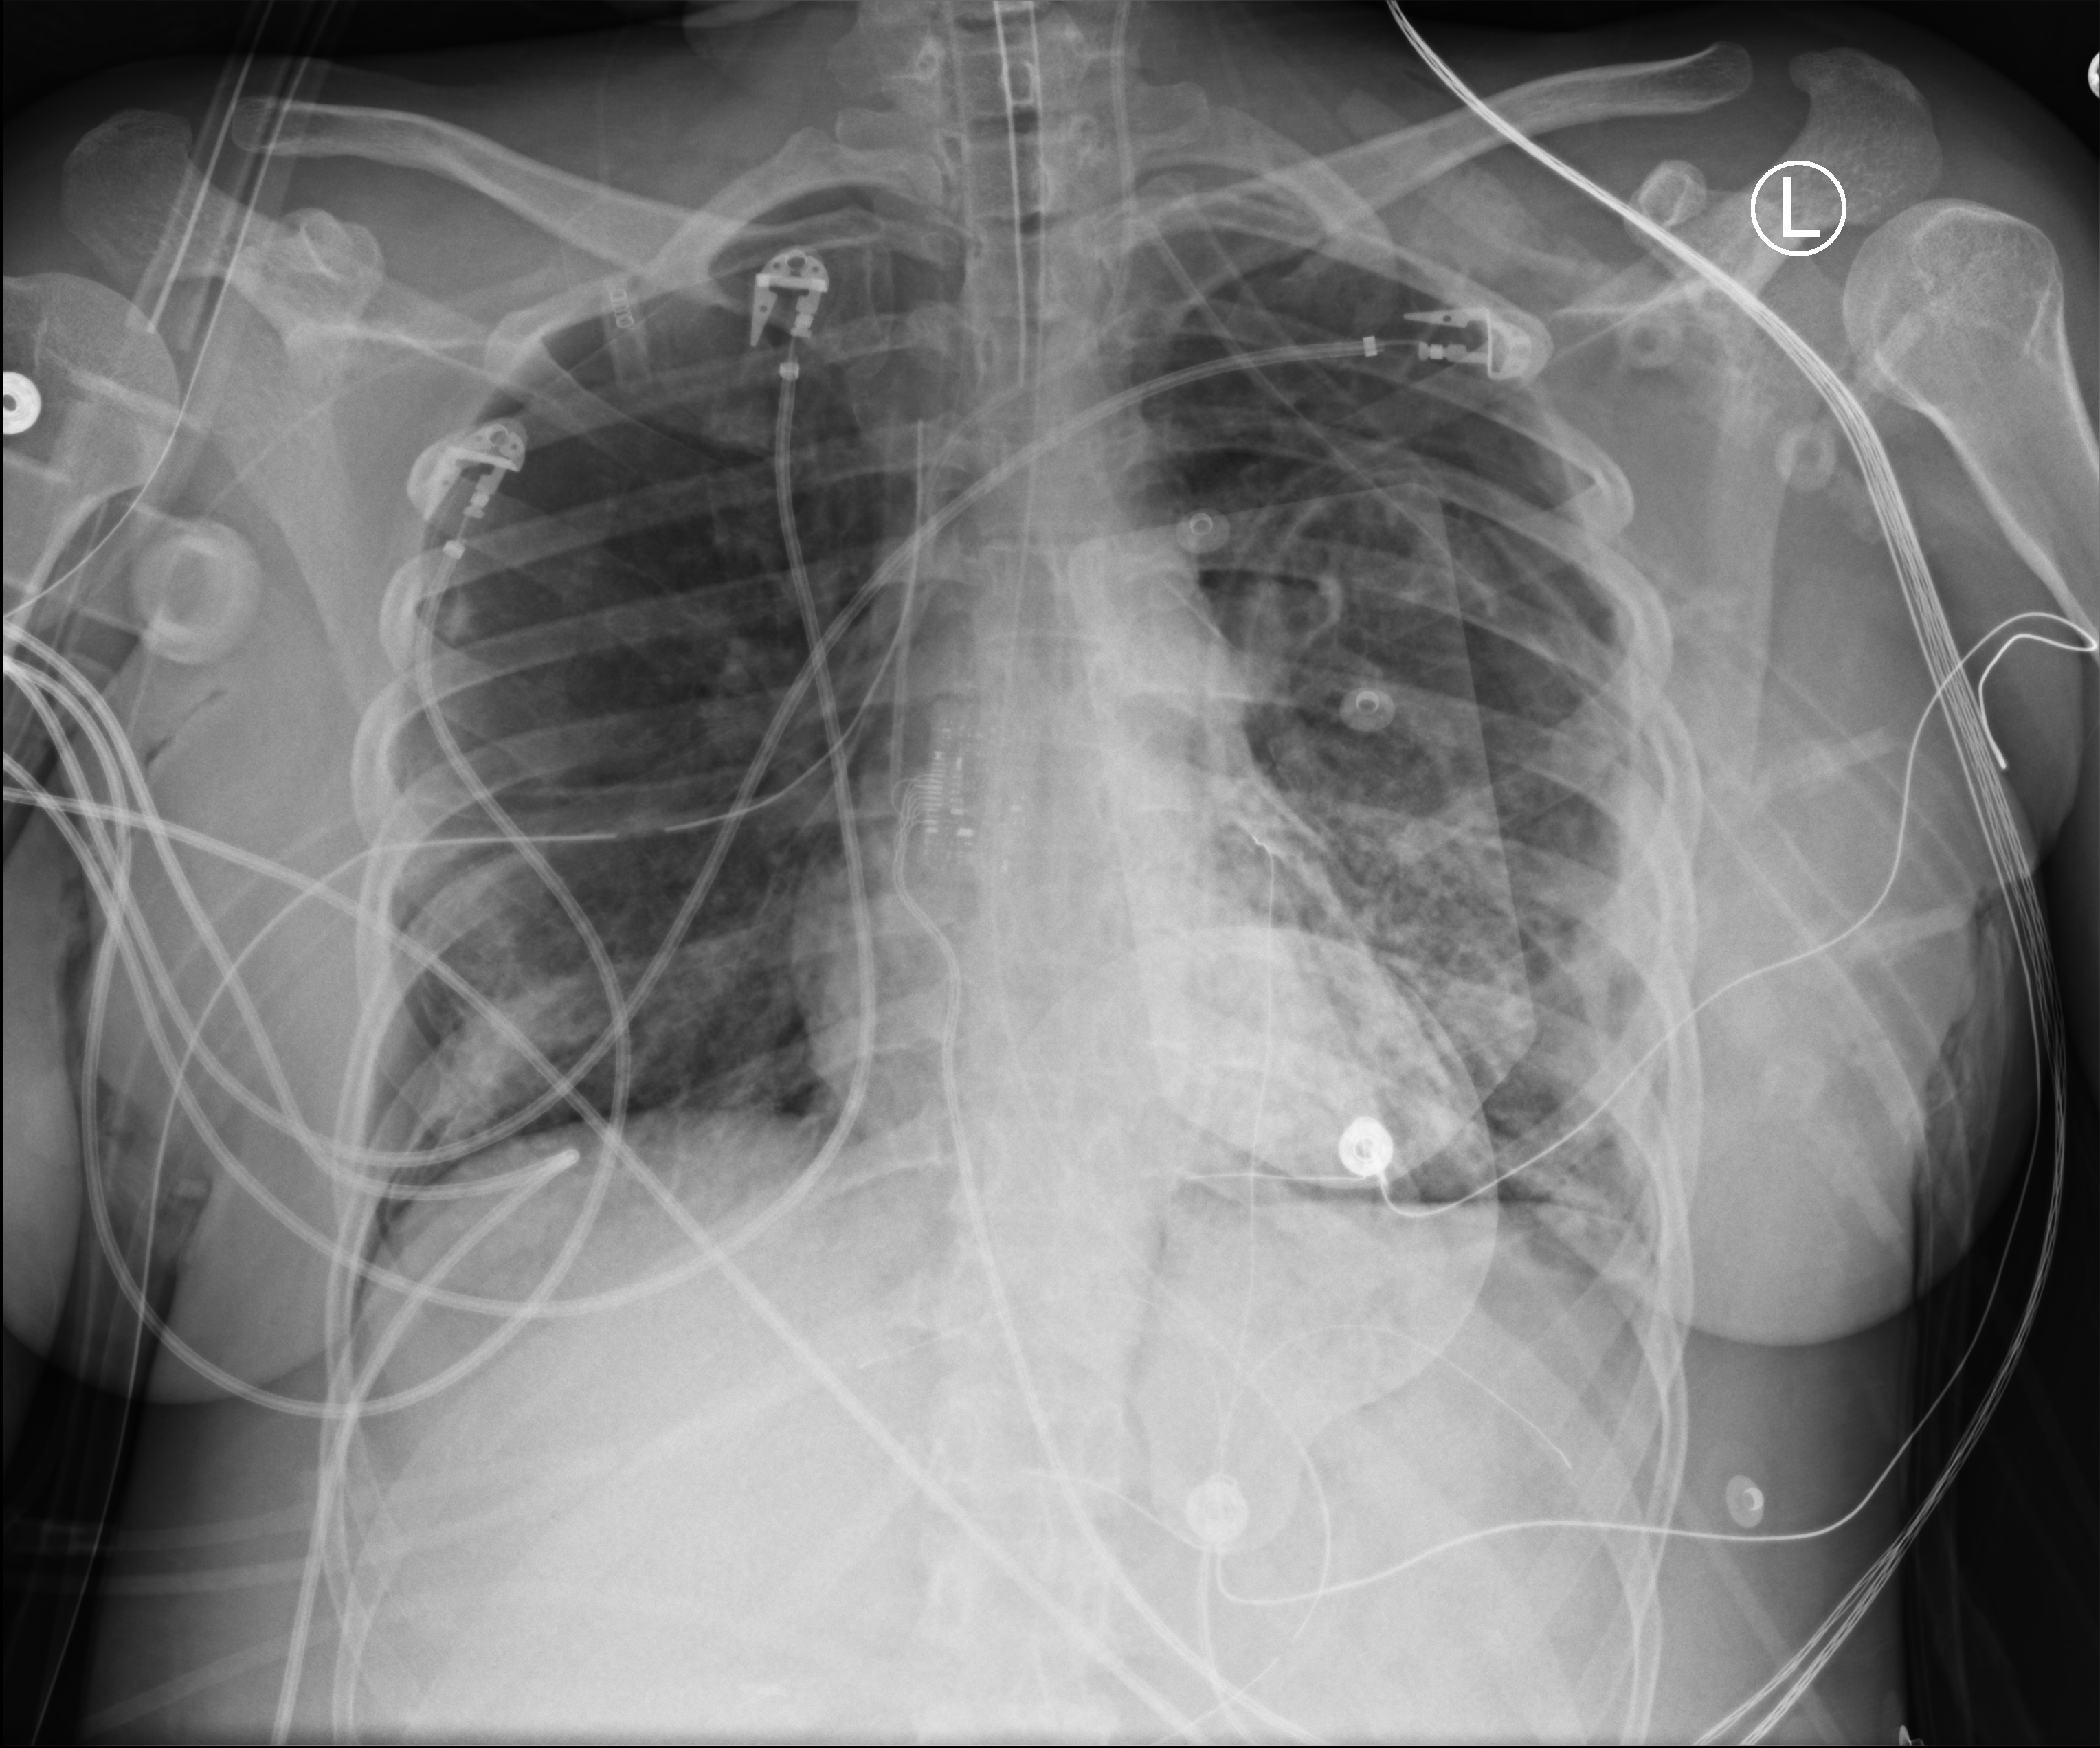
Chest X-ray (portable). Patient hospitalised with COVID-19, aged 18–59 years.
From the hospital-stay record, not from the radiograph (when in the stay this image was taken is not recorded): admitted to intensive care during this hospital stay: yes; COPD (admission record): no.